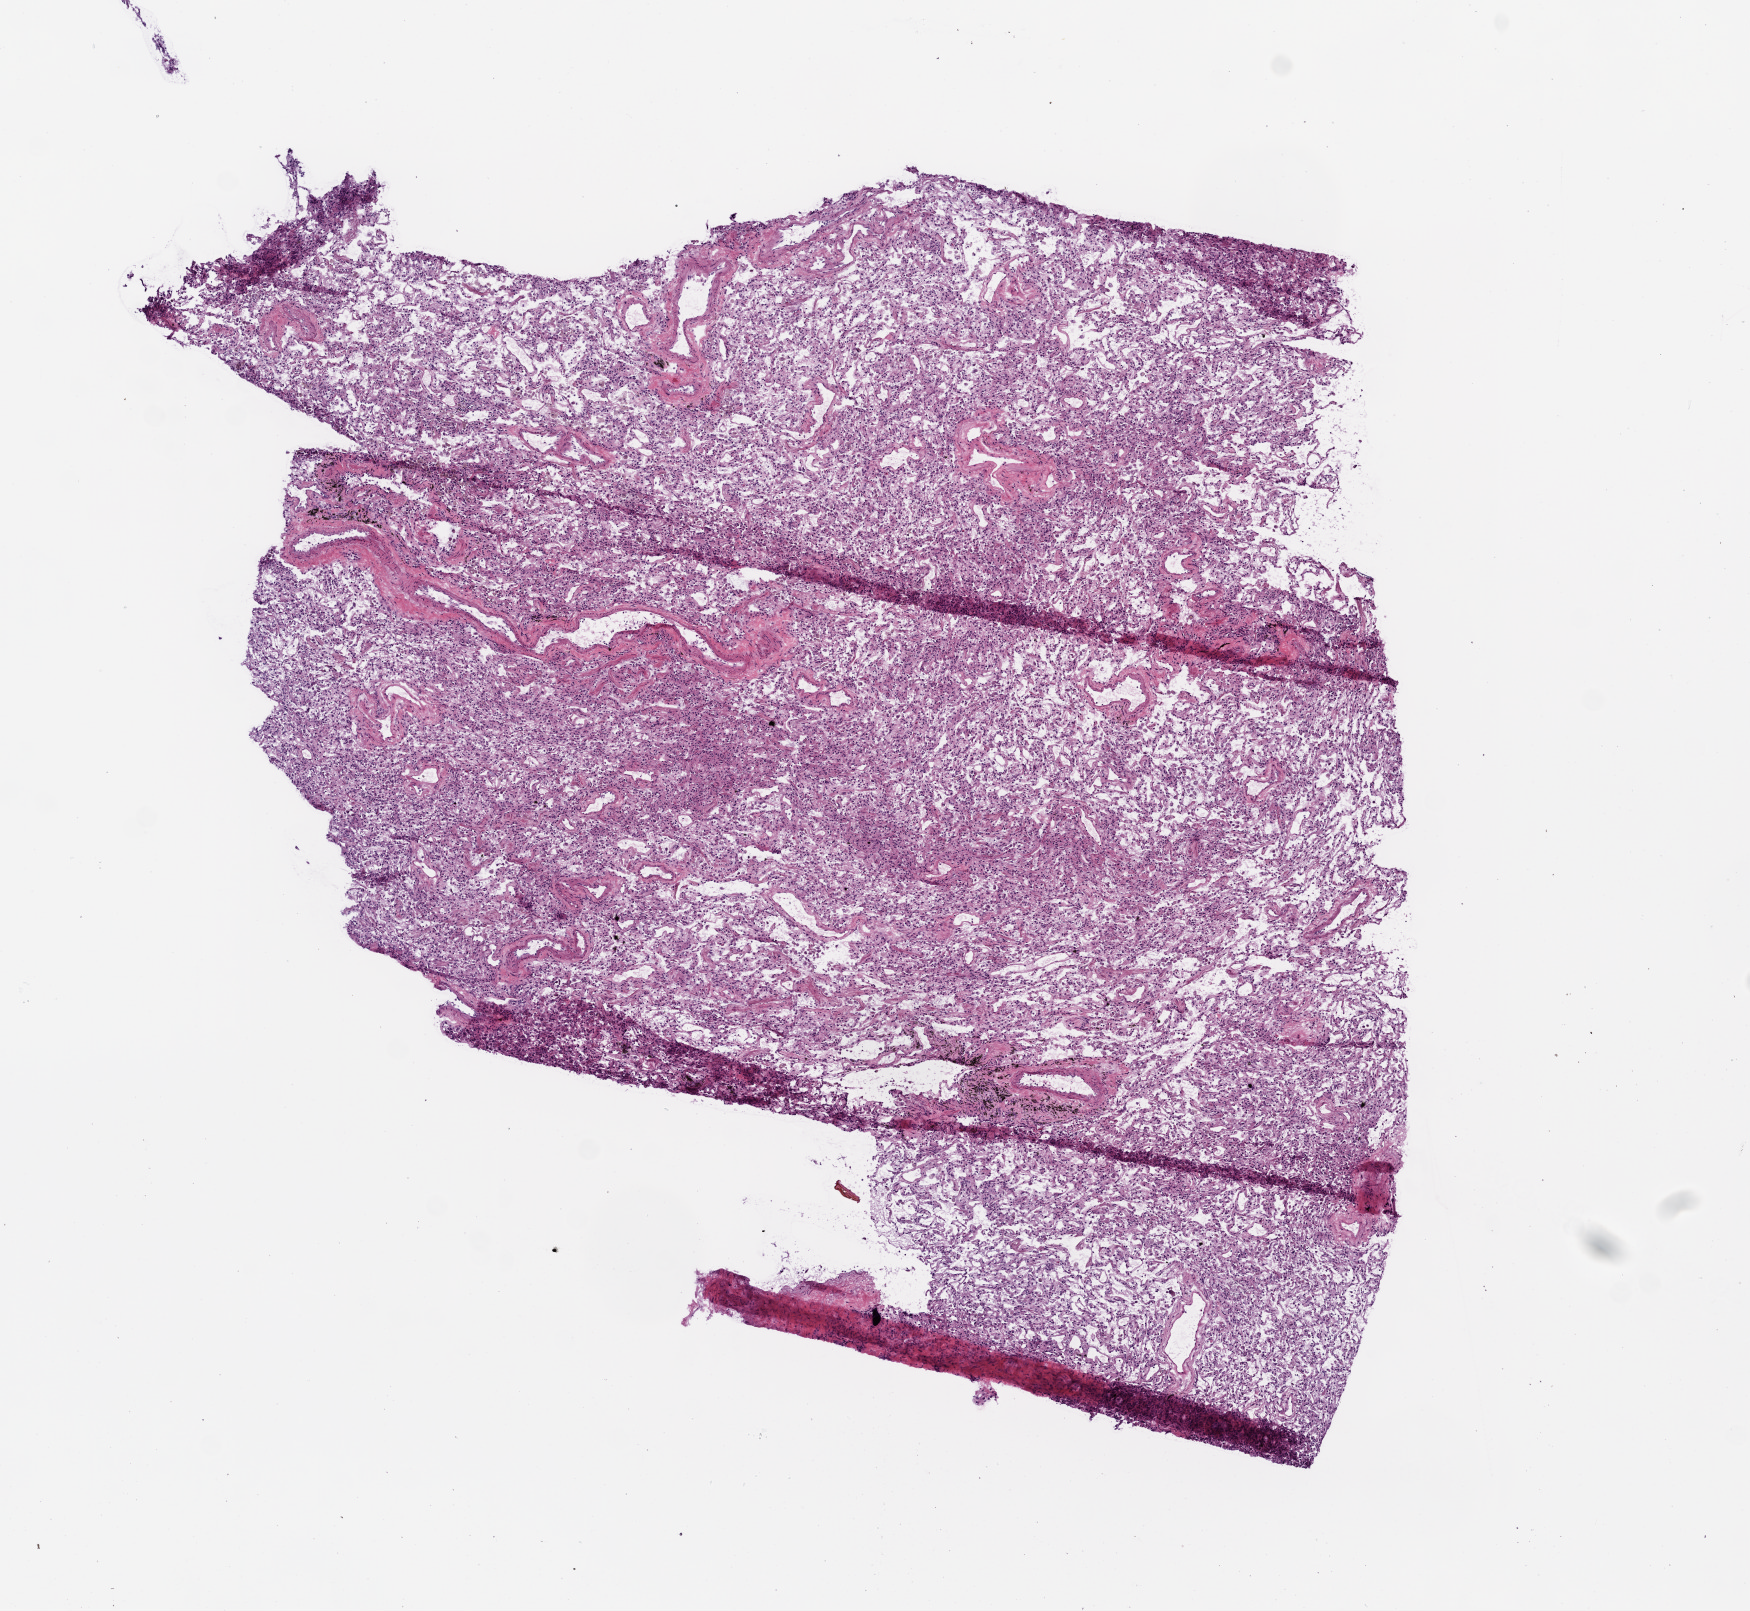
Whole-slide histology image, Hematoxylin and eosin (H&E) stained — low-resolution overview of the scanned area, about 7.0 x 6.5 mm (slide scanned at 20x), frozen section from the top of the tissue portion, sample: solid tissue normal (non-tumour tissue), lung. Male, age 74 years at initial diagnosis.
This section: solid tissue normal (non-tumour) sample from the same patient. Patient diagnosis: Squamous cell carcinoma, NOS (lower lobe, lung).